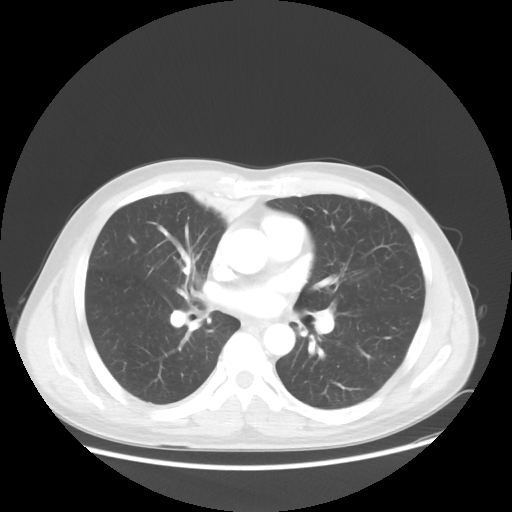
Chest CT, one axial slice. Lung window (W 1500 / L -600 HU). 512 × 512 image matrix. Patient: male, 60 years. Case-level facts recorded for this patient, not image findings: clinical TNM (as recorded): T2a N1 M0.
Annotated regions visible in this slice (bounding box drawn by a radiologist):
- lung tumour (recorded histology: squamous cell carcinoma): bounding box [x1, y1, x2, y2] px = [186, 181, 267, 233]